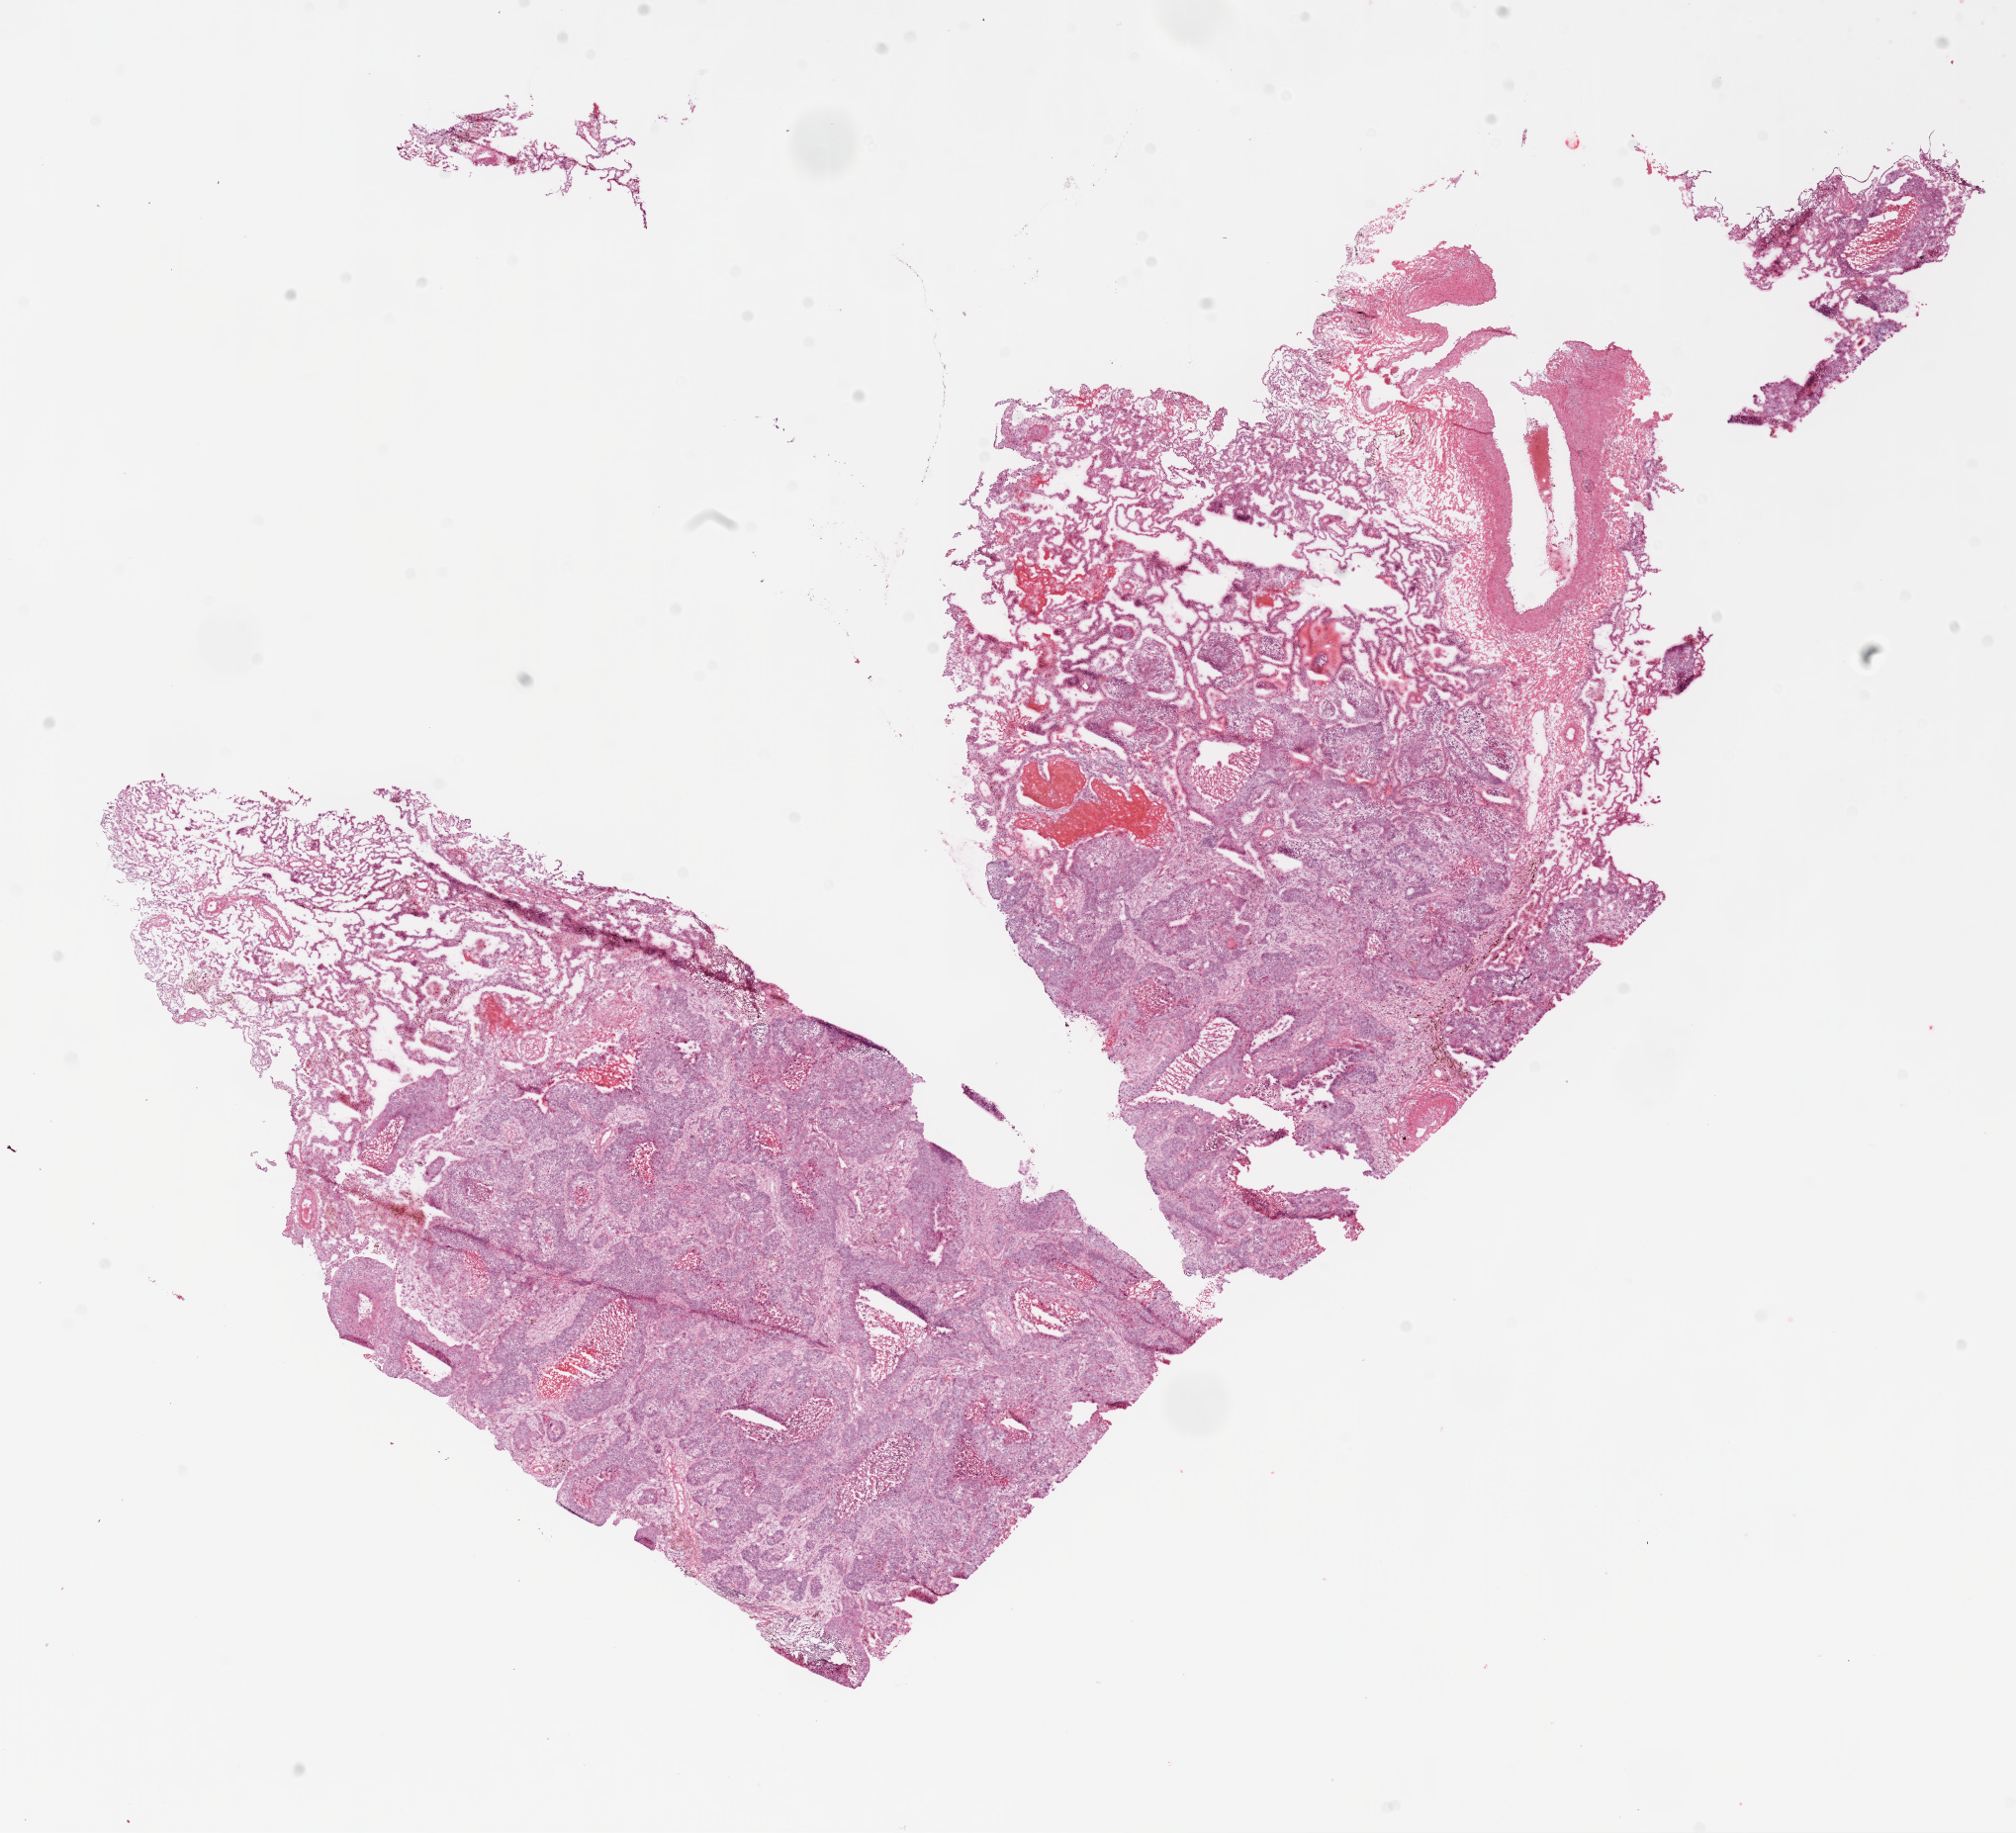
H&E whole-slide image — shown as a low-resolution overview of the whole scanned area (about 16.4 x 14.9 mm, acquisition: 20x scan), frozen section from the top of the tissue portion, sample: primary tumour, lung. Male, age 65 years at initial diagnosis. Composition of this section per pathologist review: tumour nuclei 60%, necrosis 5%.
AJCC pathologic stage: IB. Diagnosis: Squamous cell carcinoma, NOS. Laterality: right.